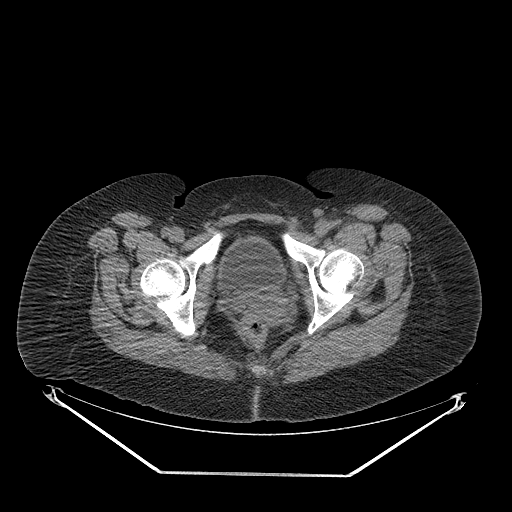
CT of an extremity soft-tissue mass (from a PET/CT study), one axial slice; position 58 of 267 along the scan axis; soft-tissue window (W 400 / L 40 HU); 3.75 mm slice thickness; 512 × 512 image matrix. Female patient. From the clinical record (not read from this slice): histological type: myxofibrosarcoma; grade: intermediate; site of the primary tumour: left thigh.
Structures marked on this image (expert contour drawn on MRI and transferred to this co-registered scan by the dataset authors):
- gross tumour volume including surrounding oedema: bounding box <288,226,353,248> (left, top, right, bottom; pixels)